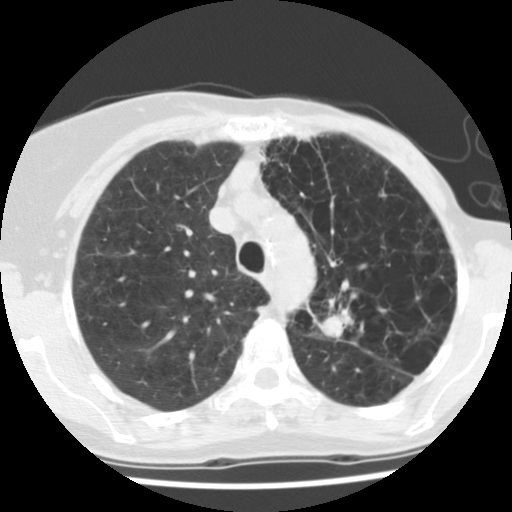
Low-dose screening chest CT, one axial slice; position 96 of 128 along the scan axis; reconstruction kernel STANDARD; 140 kVp; lung window (W 1500 / L -600 HU); 2.5 mm slice thickness; 512 × 512 image matrix, field of view 290 × 290 mm.
Annotated regions visible in this slice (manually delineated by an expert):
- lesion 1 (tumor, upper lobe of left lung): bounding box <318,310,354,340> (left, top, right, bottom; pixels)